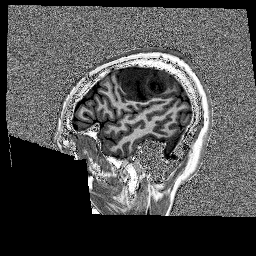
Brain MRI from a brain-tumour surgery series, one sagittal slice; slice 38 of 176 in the series (ordered by position); 256 × 256 image matrix, field of view 256 × 256 mm. From the clinical record (not read from this slice): histopathology: Glioblastoma; WHO grade: 4; IDH mutation: no.
Structures marked on this image (manually delineated by an expert):
- tumour: box from (x=118, y=65) to (x=175, y=101) px